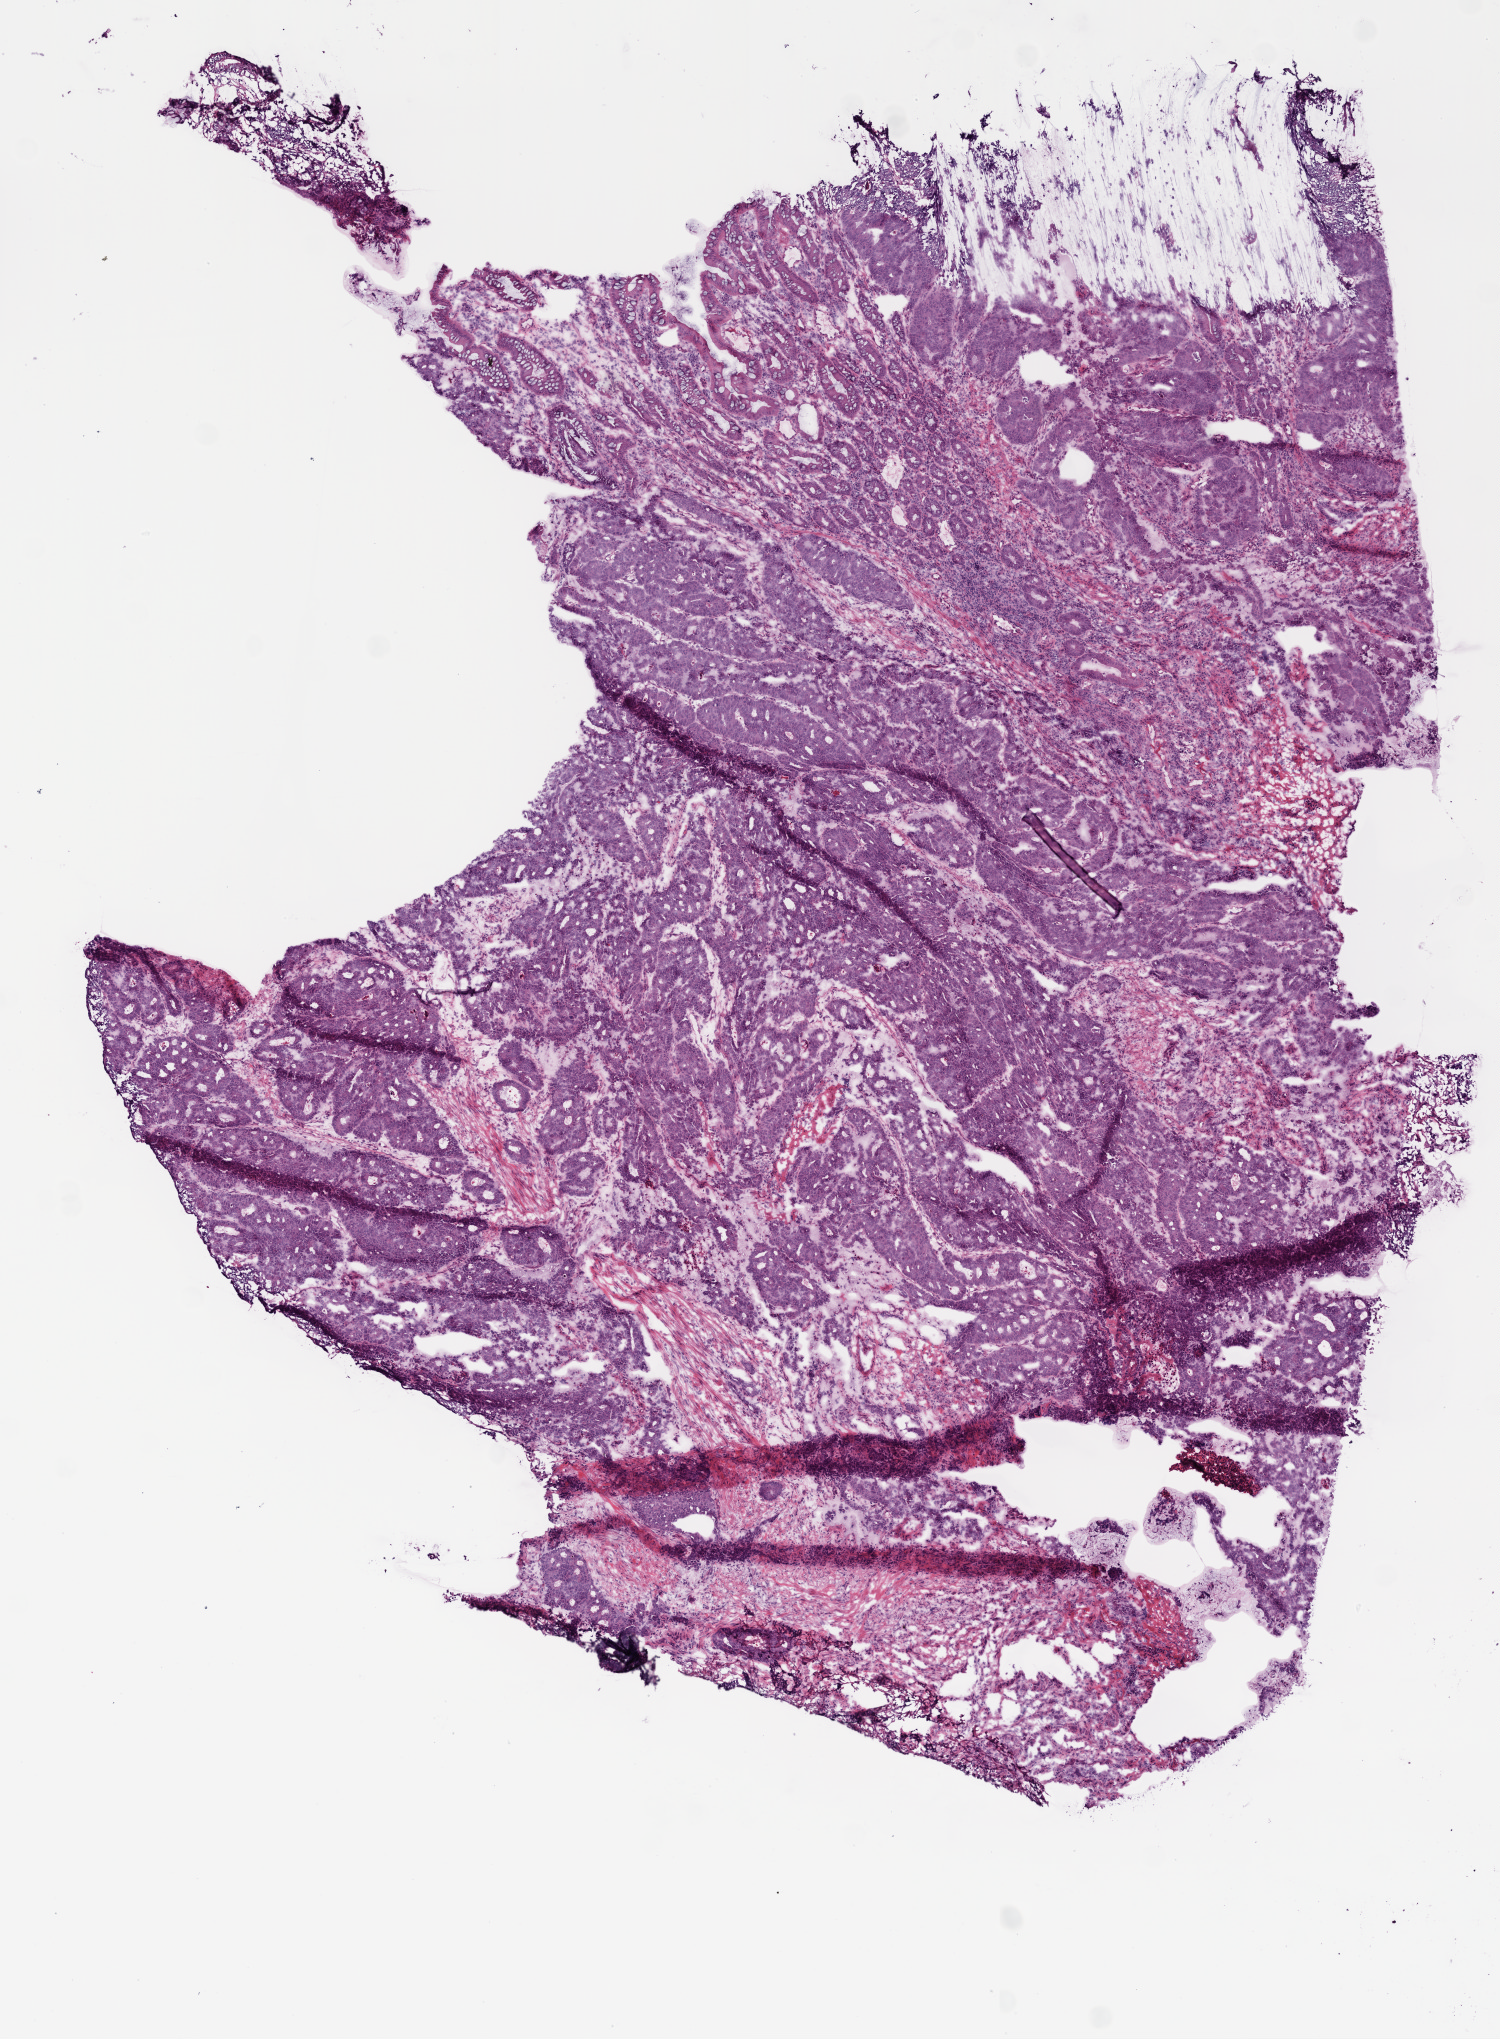
Whole-slide histology image, H&E — a low-resolution overview of the entire scanned area, about 6.0 x 8.2 mm (from a 20x scan), frozen section from the bottom of the tissue portion, primary tumour sample from the colon. Male, age 59 years at initial diagnosis. Slide review estimates, as recorded: tumour cells 75%, tumour nuclei 70%, normal cells 5%, stromal cells 15%, necrosis 5%.
Histologic diagnosis: Adenocarcinoma, NOS. AJCC pathologic stage: IV. TNM: T3 N2 M1. Lymph nodes positive (case pathology): 5 of 12 examined.